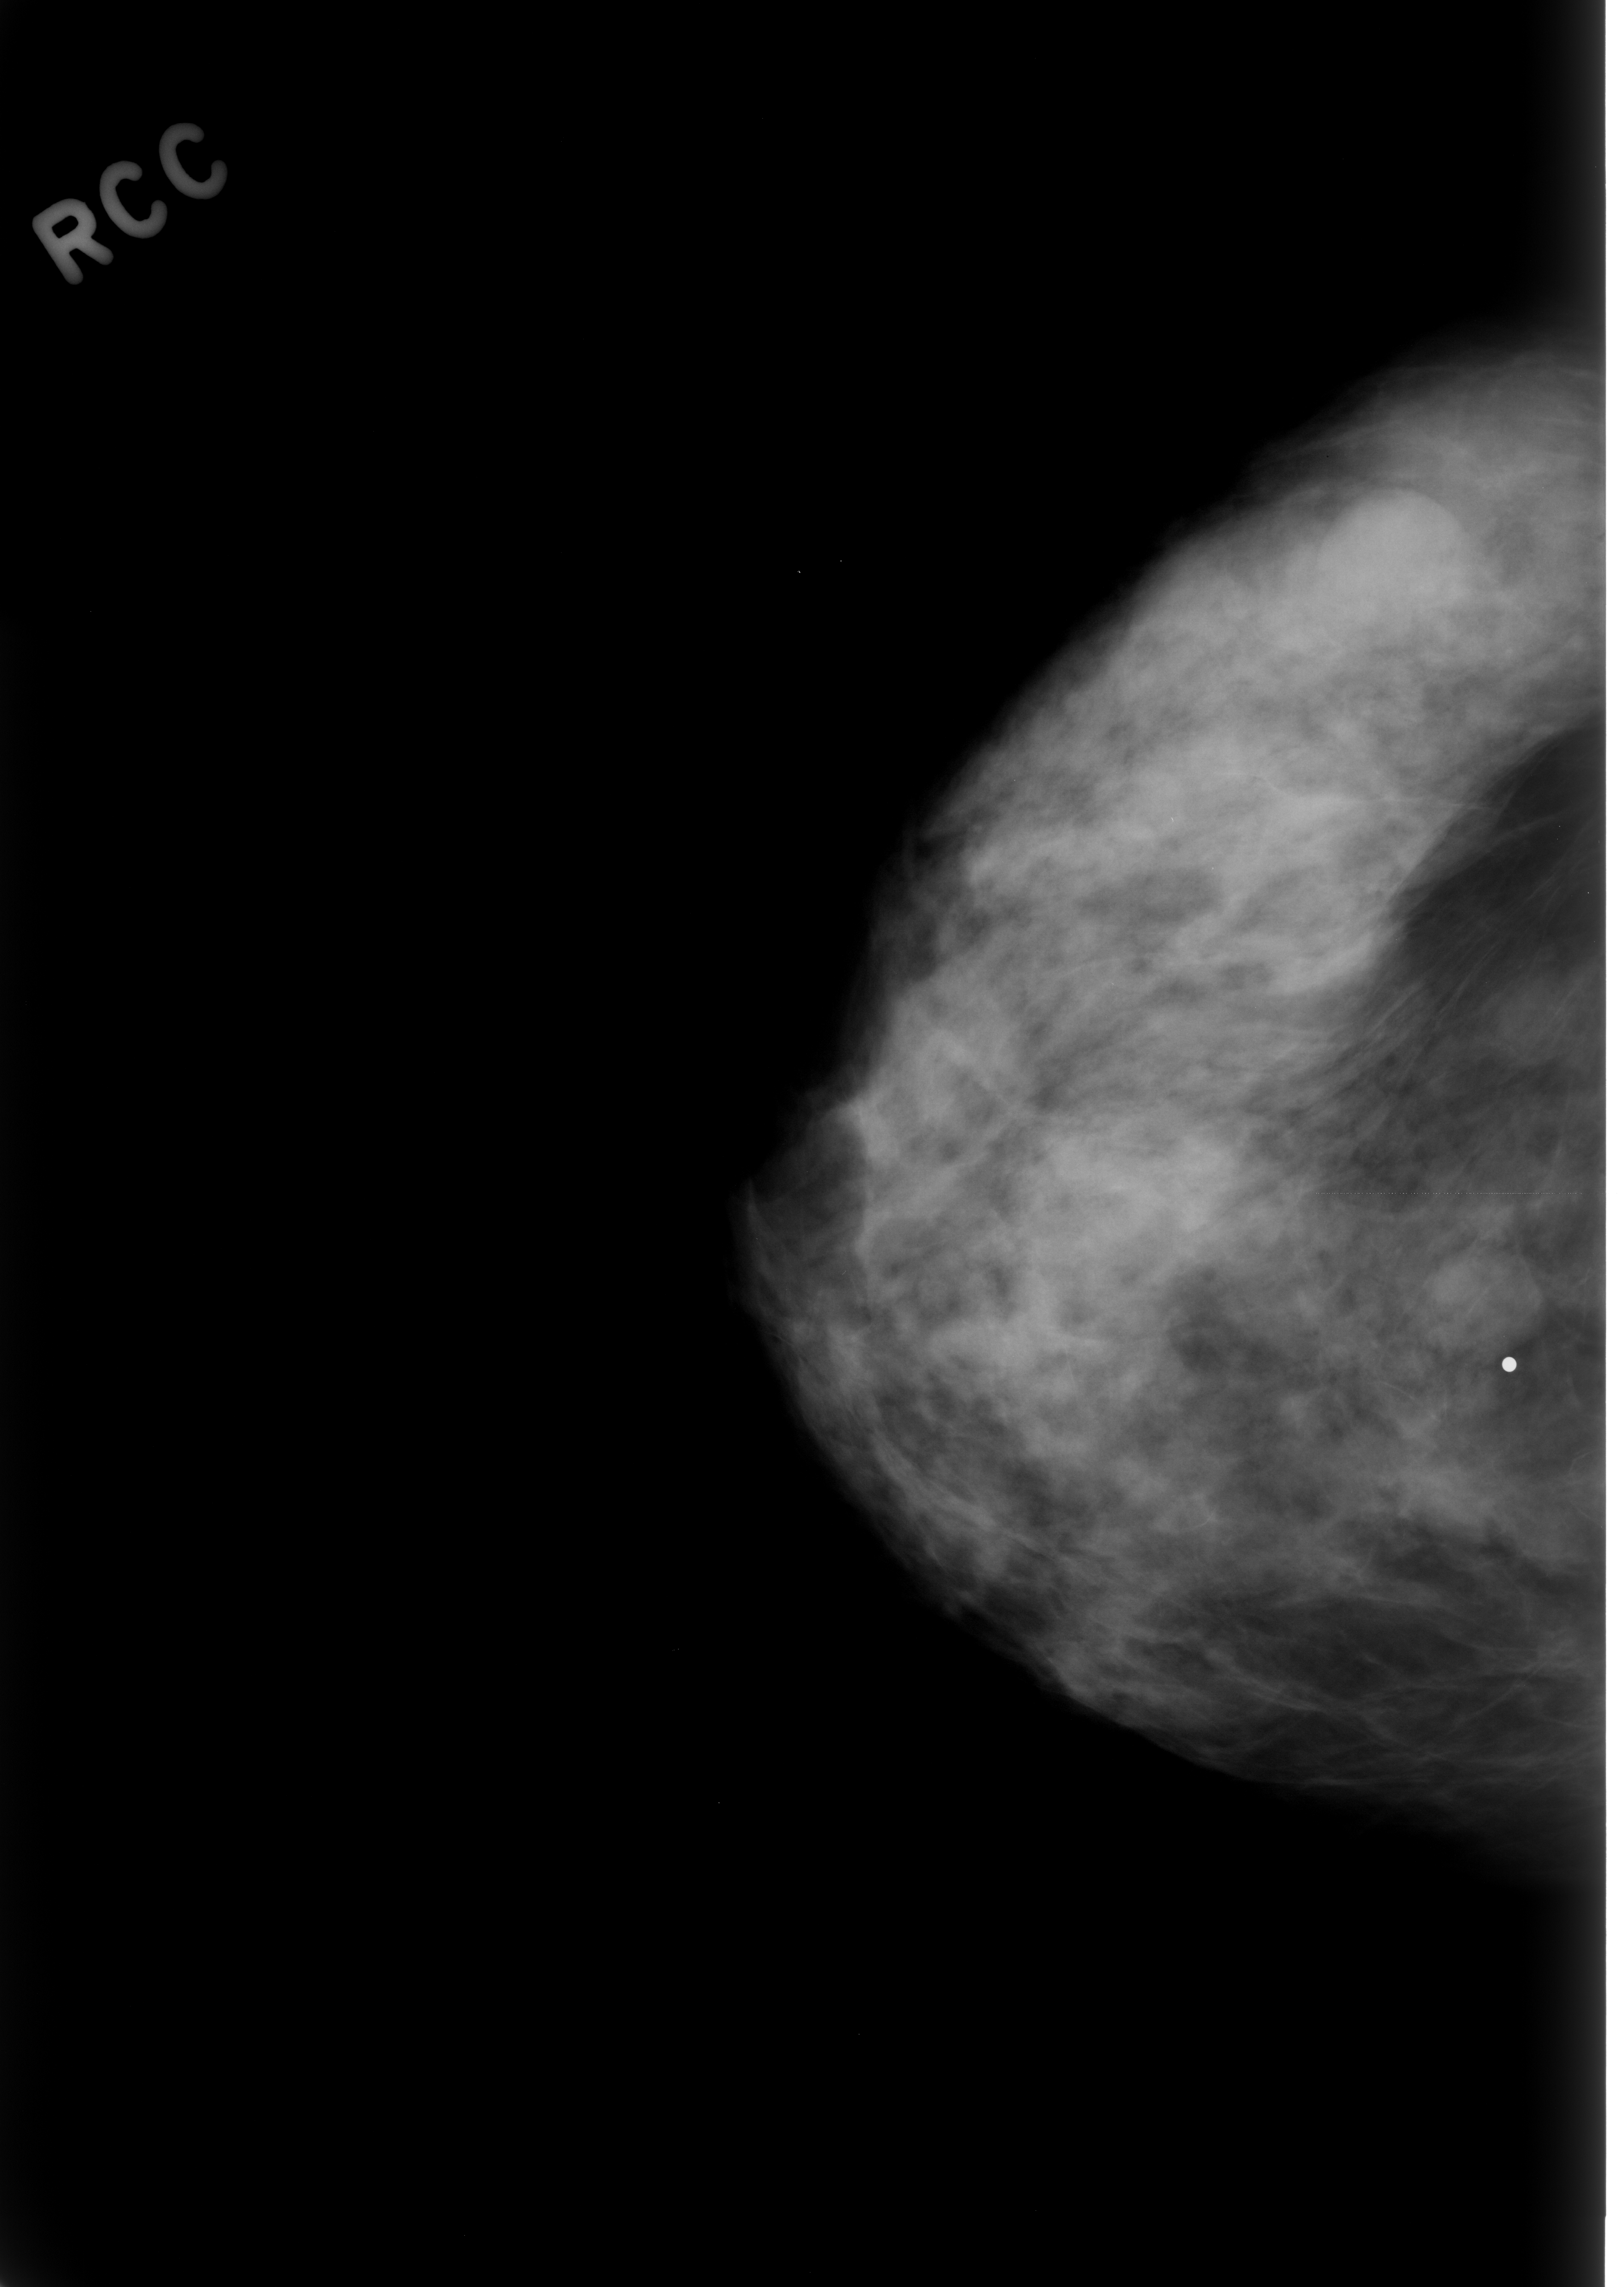
Digitized screen-film mammogram; right breast; craniocaudal (CC) view; breast composition: heterogeneously dense (BI-RADS density category 3 of 4); 1624 × 2287 image matrix.
Expert-marked regions of interest on this image (one box per marked abnormality):
- mass, shape oval, margins obscured; BI-RADS assessment category 3; subtlety rating 5 on a 1 (subtle) to 5 (obvious) scale; pathology result (as recorded, not read from the image): benign: bounding box <1300,479,1474,641> (left, top, right, bottom; pixels)